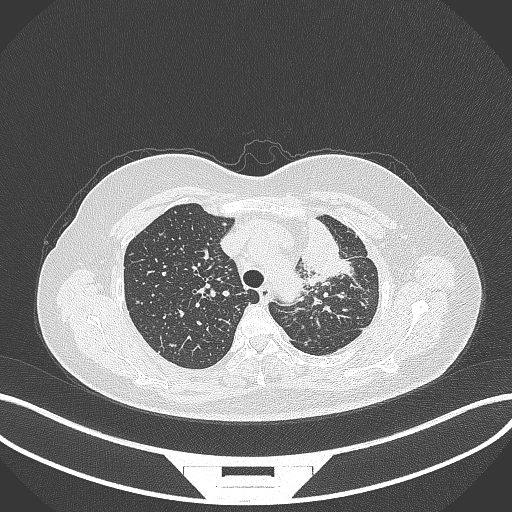
Chest CT, one axial slice. Position 258 of 348 along the scan axis. Reconstruction kernel B70f. 120 kVp. Lung window (W 1500 / L -600 HU). 1 mm slice thickness. 512 × 512 image matrix. Female patient, age 49 years. From the clinical record (not read from this slice): clinical TNM (as recorded): T1c N0 M1.
Annotated regions visible in this slice (rectangle marked by the reading radiologist):
- lung tumour (recorded histology: adenocarcinoma): bounding box <293,220,357,285> (left, top, right, bottom; pixels)